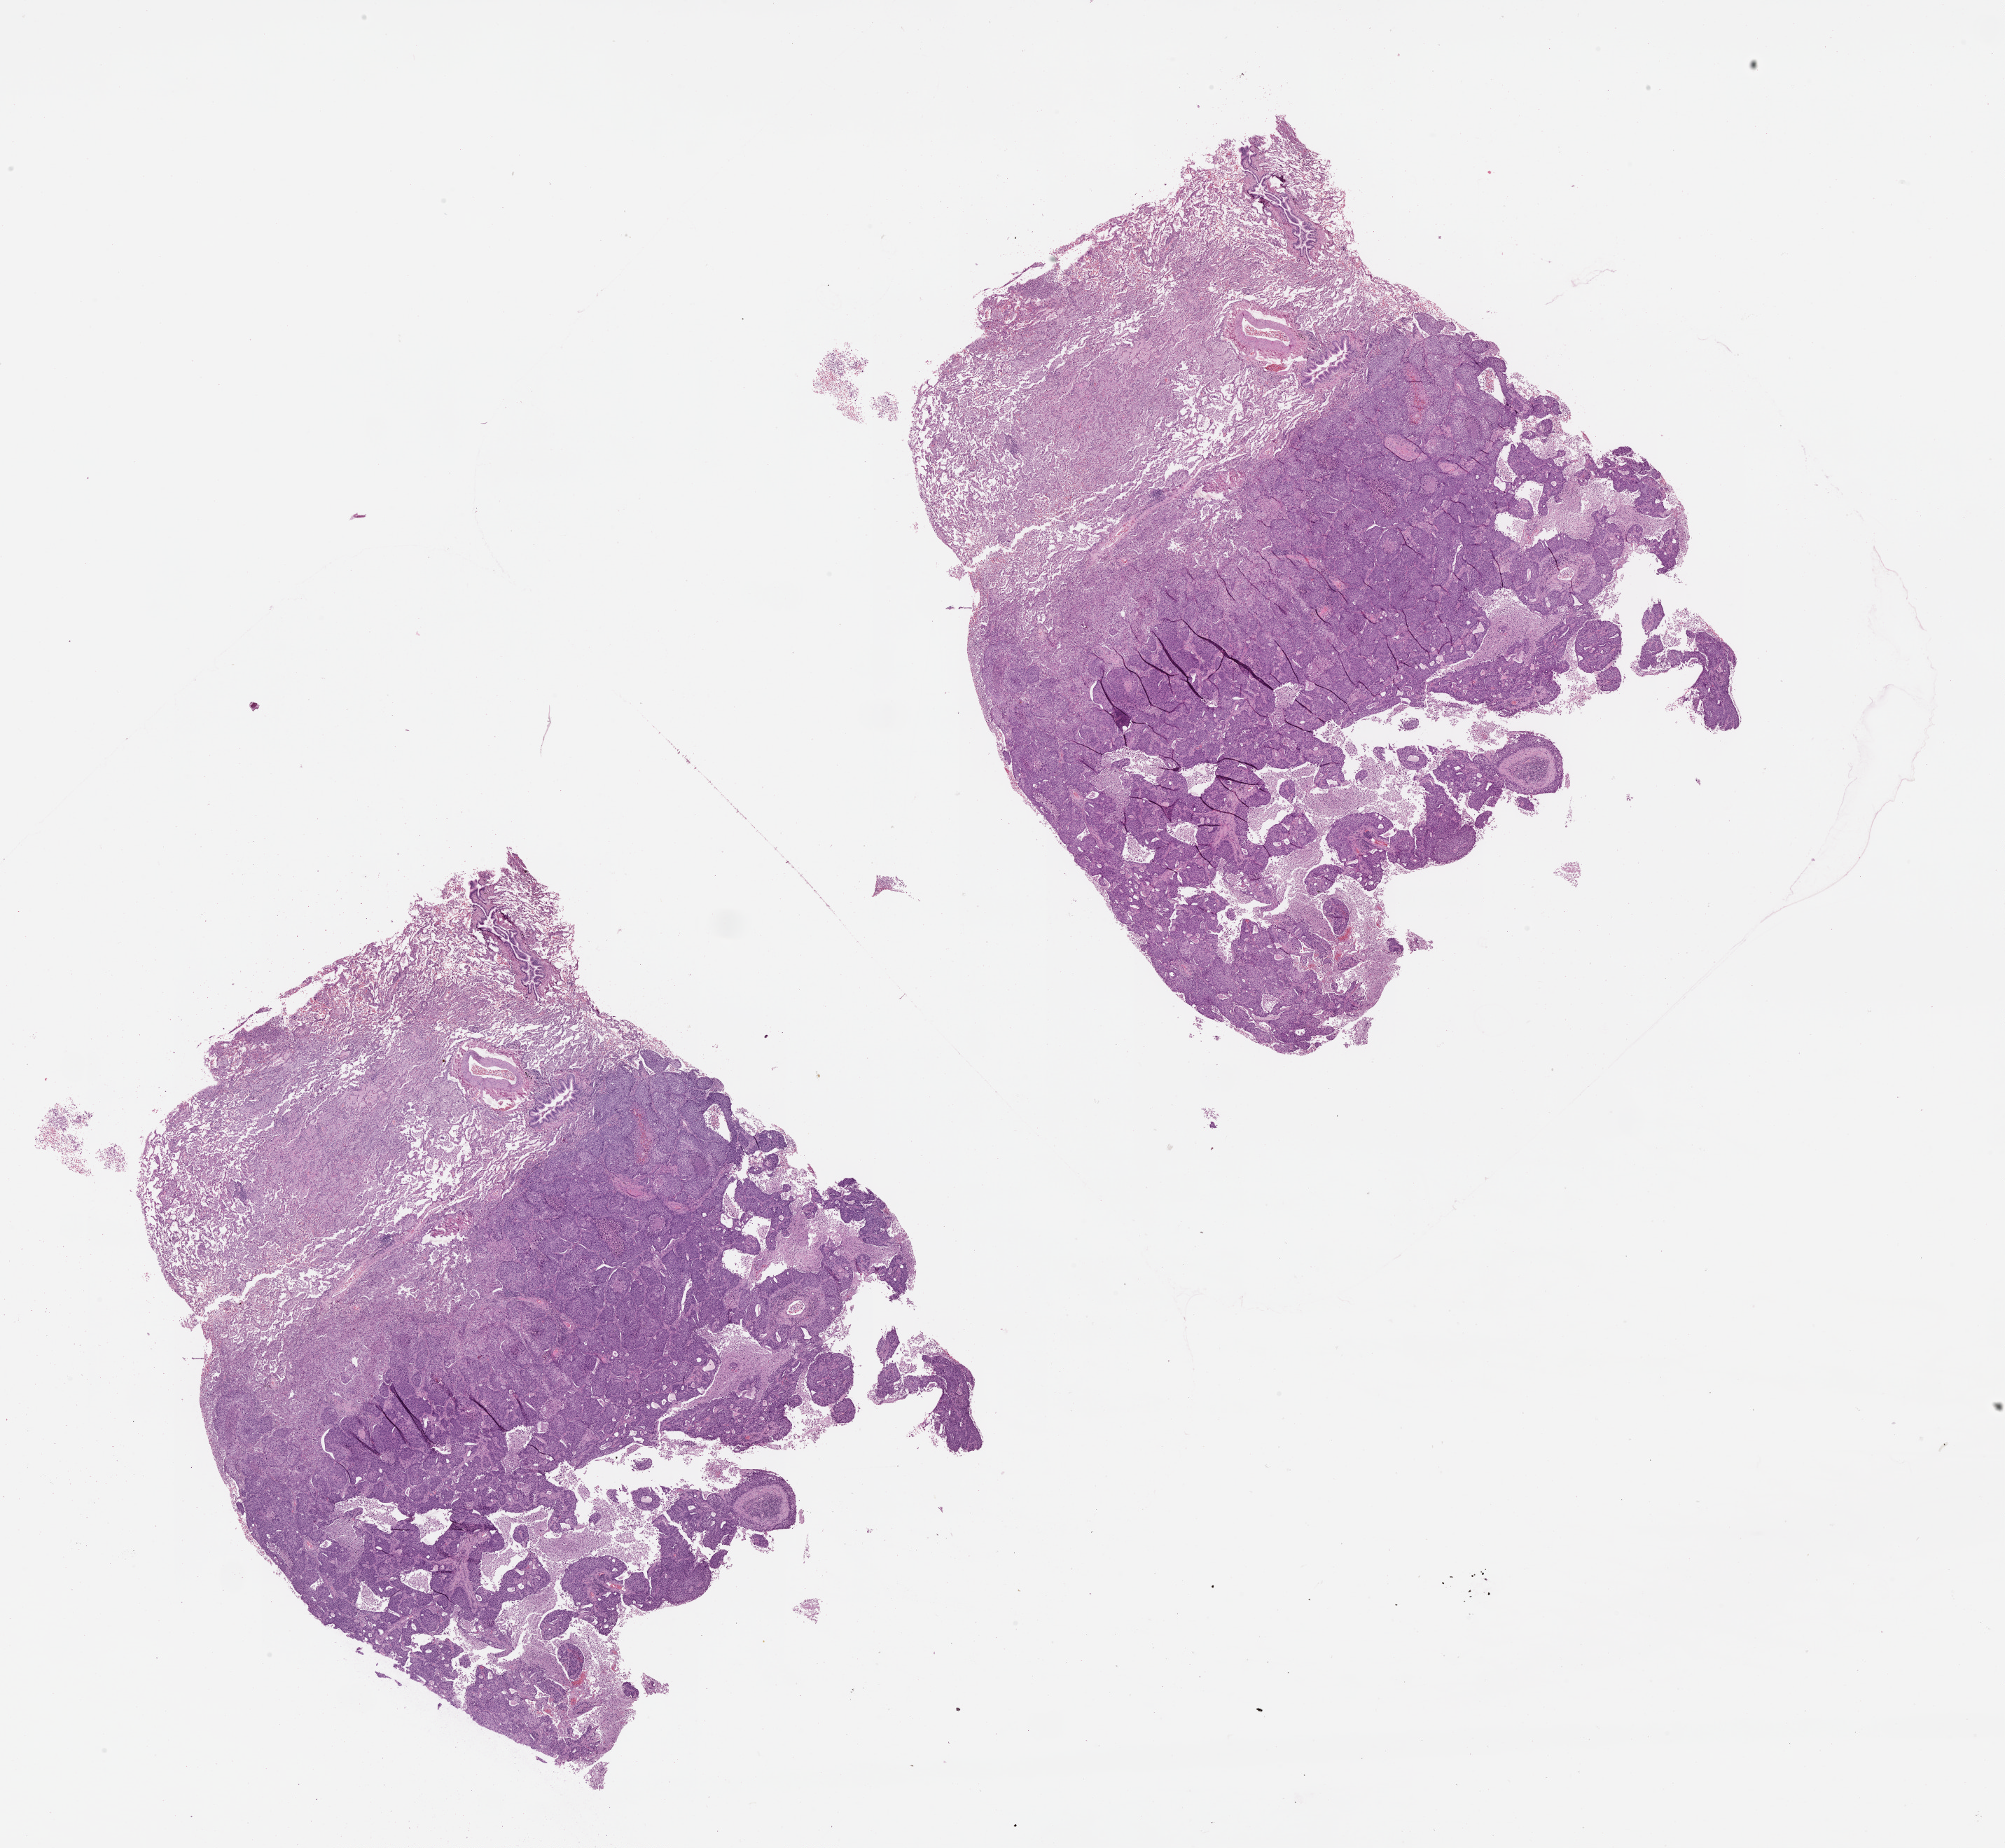
Digitized H&E tissue section (whole slide), whole scanned area (about 23.1 x 21.2 mm, from a 20x scan) shown as a low-resolution overview; tumour tissue sample, lung. 63-year-old male patient.
Patient diagnosis (cohort enrolment): squamous cell carcinoma (lung).